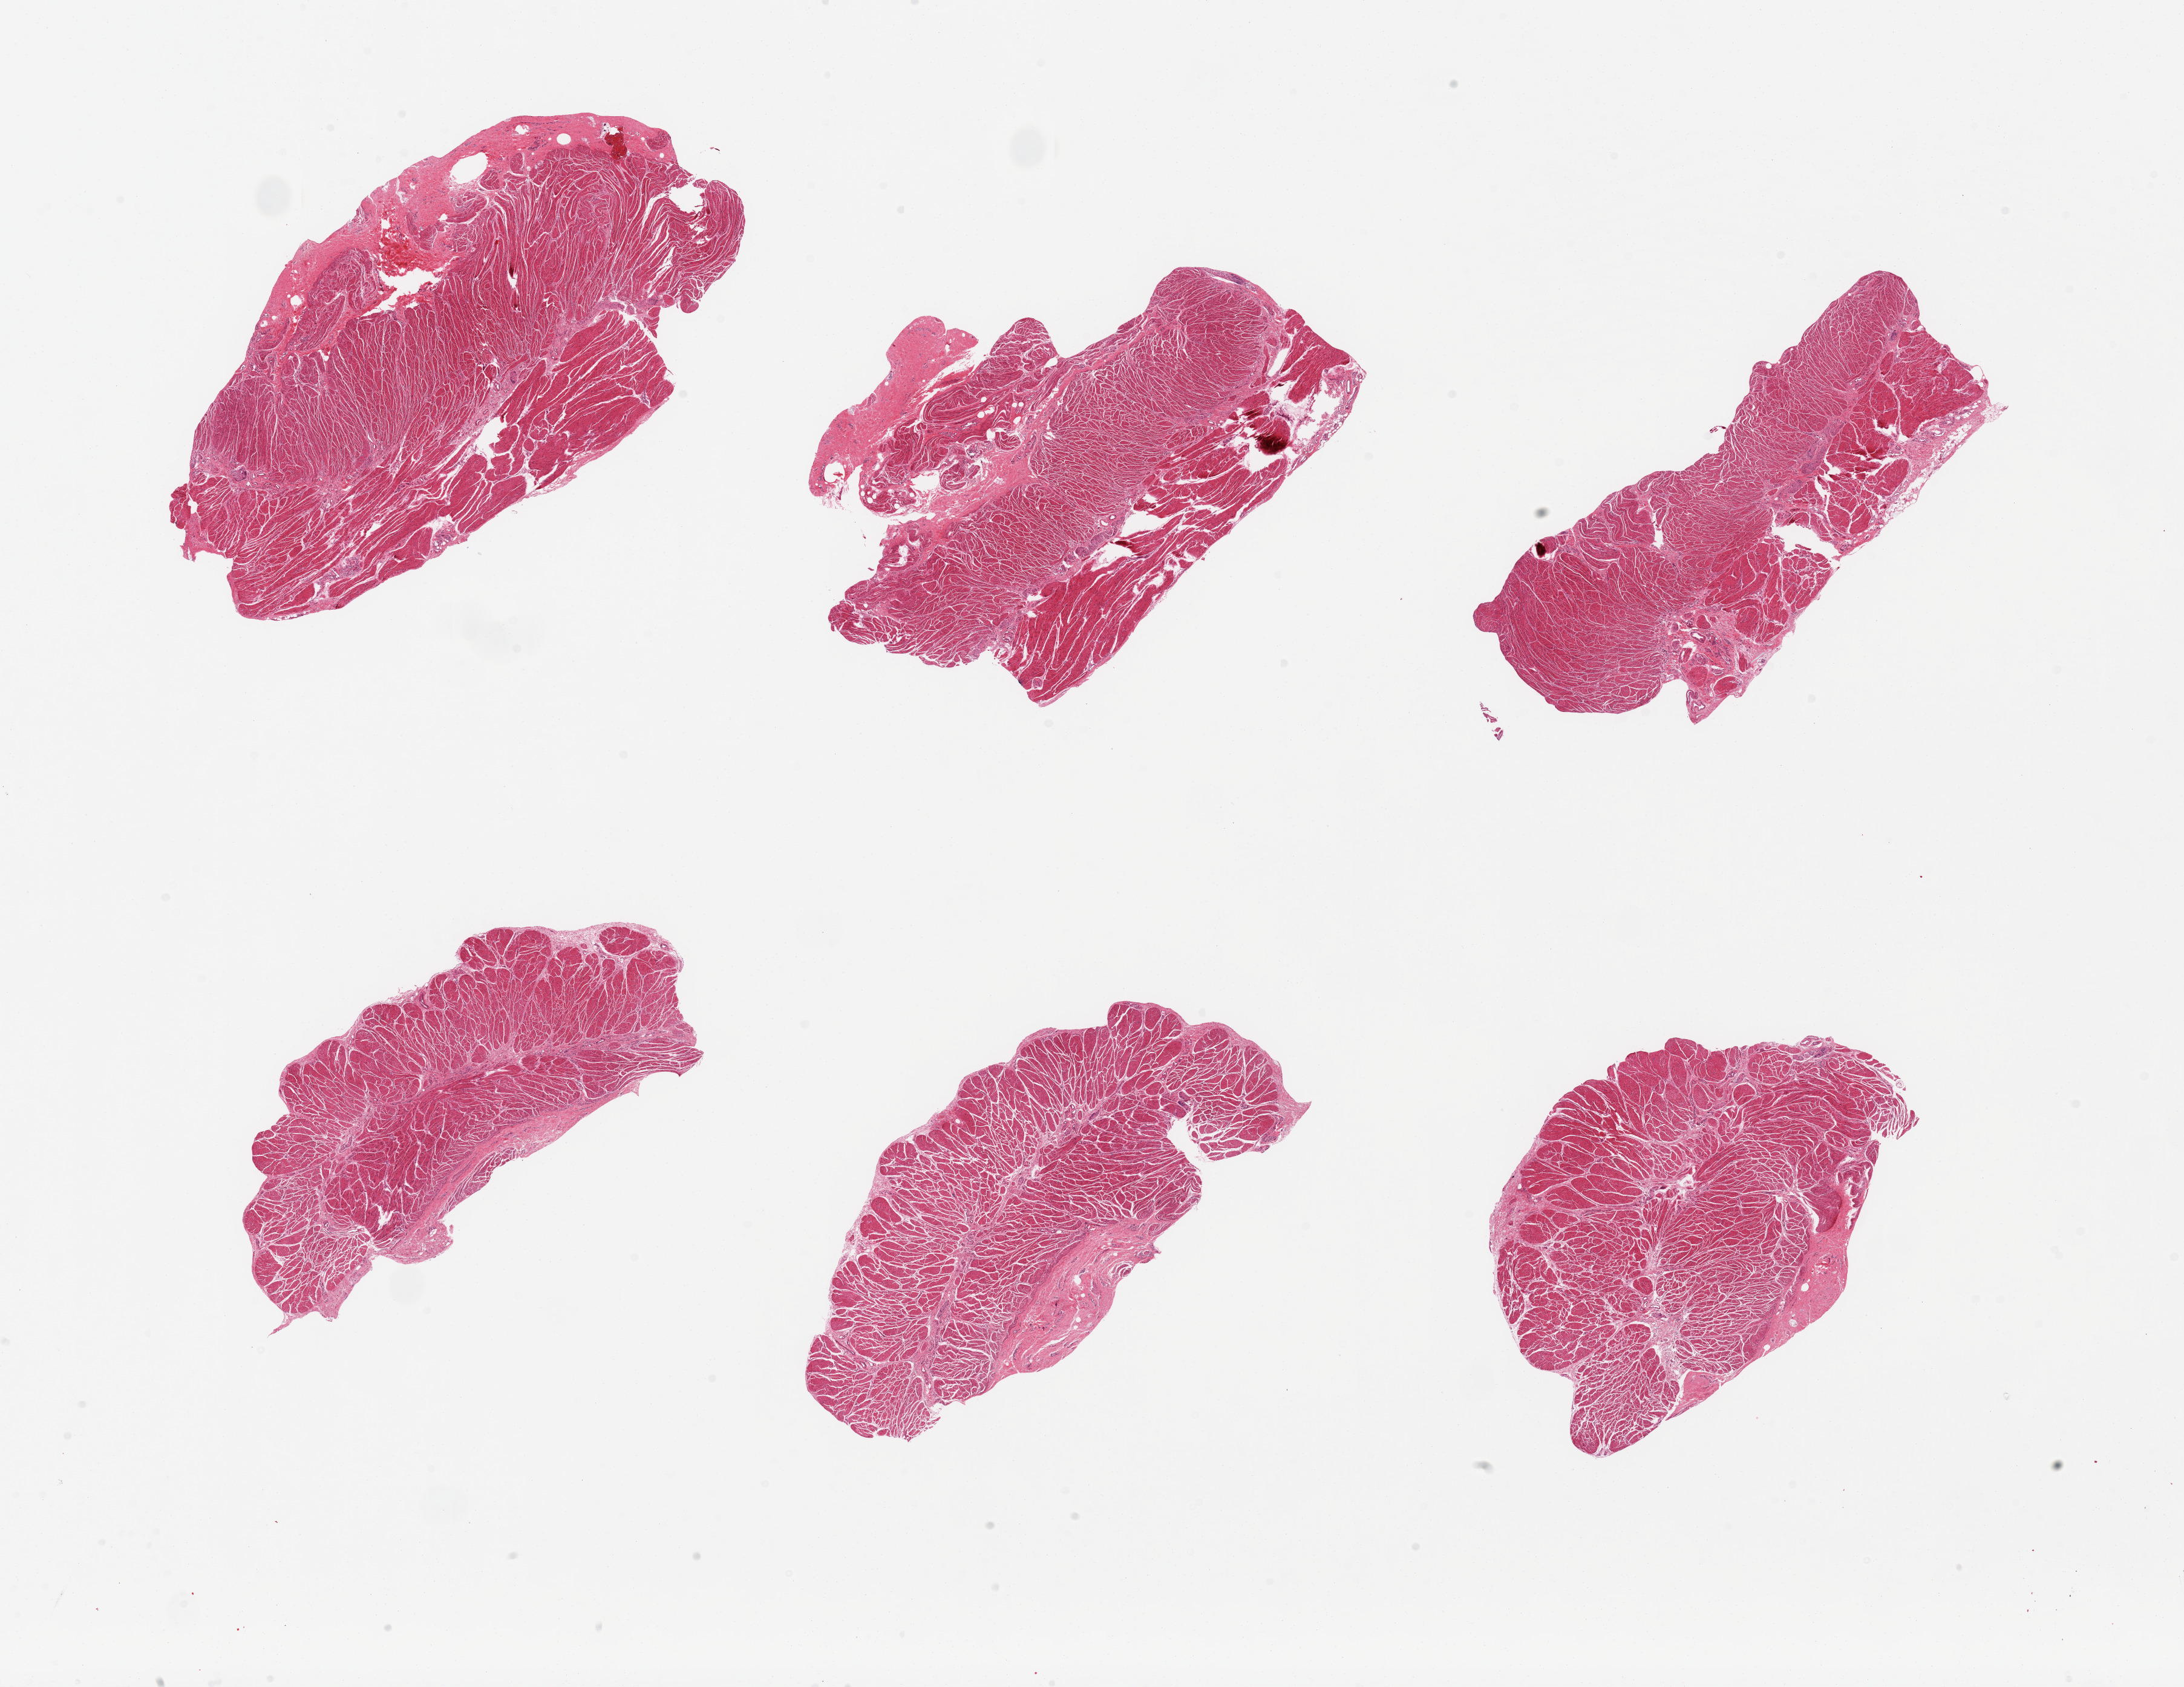
Whole-slide image, H&E stain, brightfield, whole scanned area (about 28.5 x 22.1 mm) shown as a low-resolution overview. PAXgene-fixed, paraffin-embedded tissue. Sampled site (target tissue): gastroesophageal junction. Tissue donor sample. Donor sex: female.
- pathologist's review note for this sample: 6 pieces; well trimmed muscularis